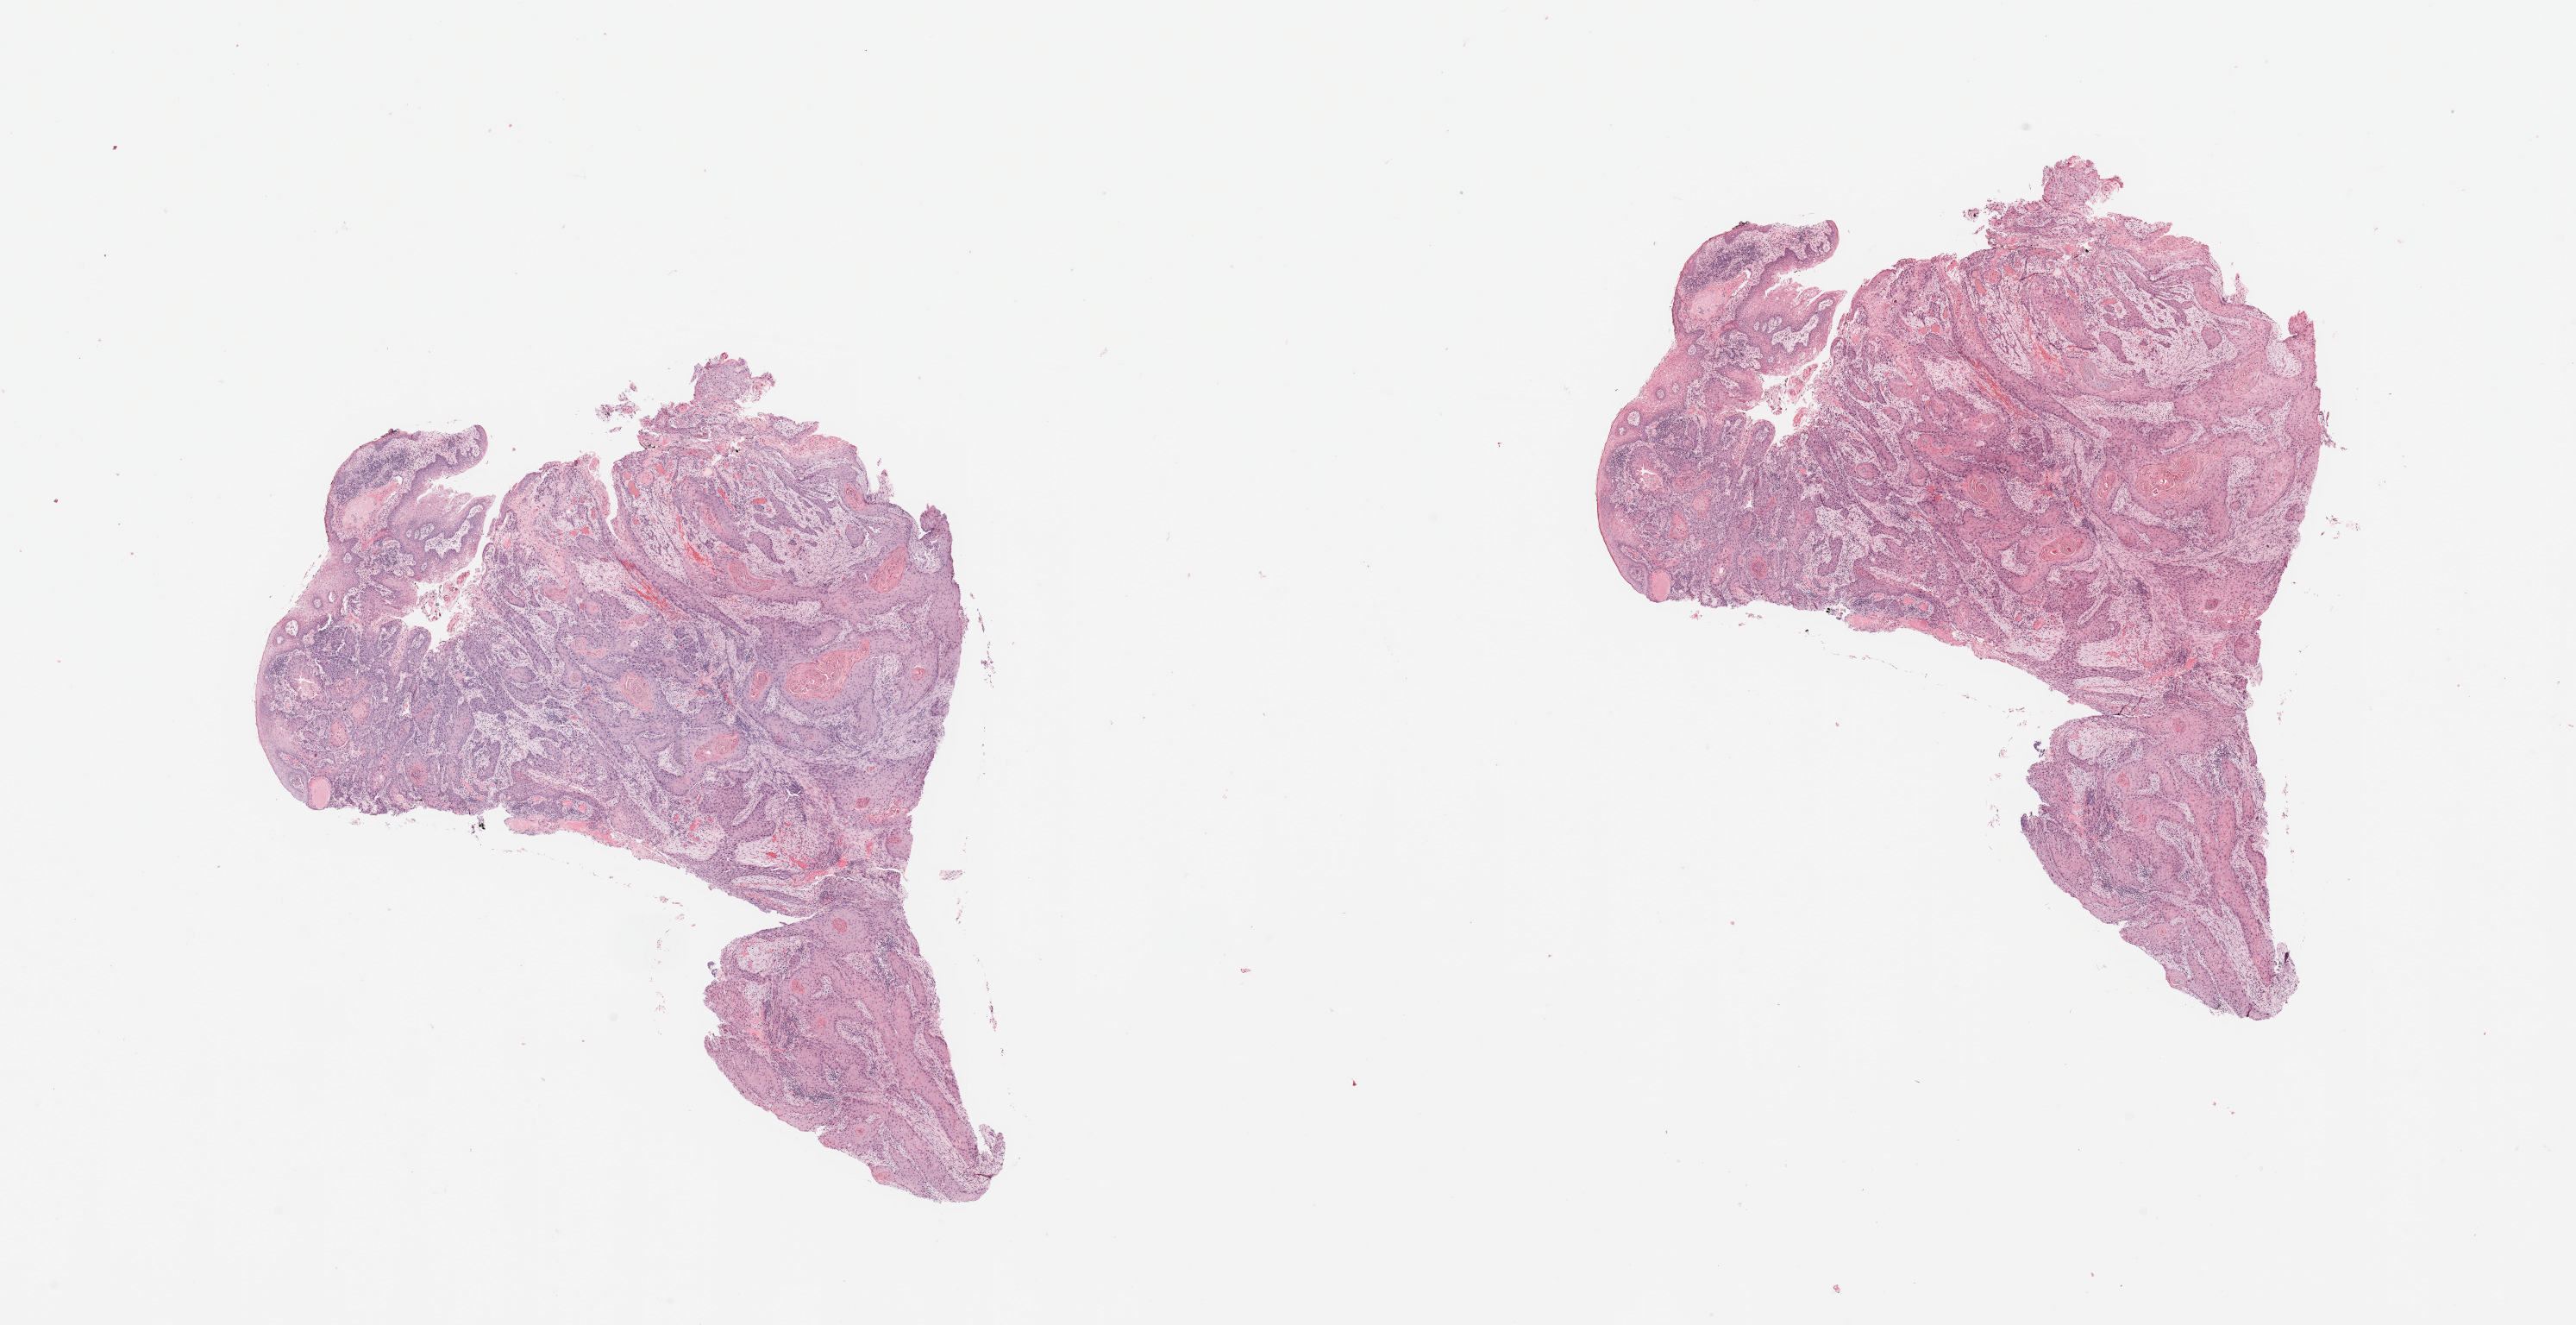
H&E-stained whole-slide image — whole scanned area (about 23.6 x 12.1 mm, slide scanned at 20x) shown as a low-resolution overview; tumour tissue sample, sampled site: oral cavity. 67-year-old female patient. Histologic grade: G2 (moderately differentiated). Pathologist review of this section (percent, as recorded): tumour nuclei 85%, necrosis 5%.
Diagnosis: Squamous cell carcinoma, NOS. Primary tumour site (as recorded): oral cavity. AJCC pathologic stage: IVB.